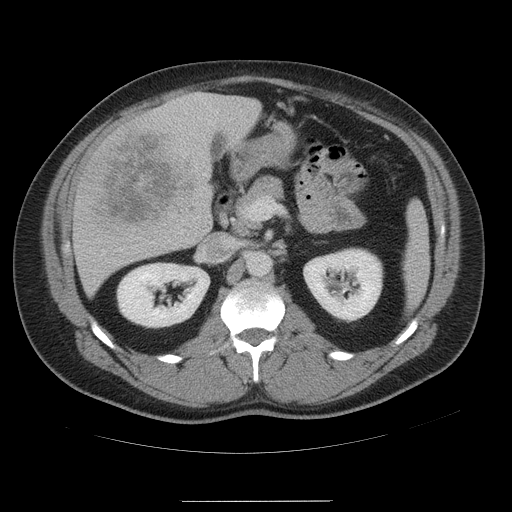
Contrast-enhanced abdominal CT, one axial slice. Position 26 of 54 along the scan axis. 120 kVp. Intravenous contrast given. Soft-tissue window (W 400 / L 40 HU). 512 × 512 image matrix, field of view 436 × 436 mm. Male patient, age 40 years. From the clinical record (not read from this slice): diagnosis: colorectal cancer liver metastases, imaged before liver resection; multiple liver metastases: no; largest metastasis: 15 cm; chemotherapy before resection: no.
Structures marked on this image (manually delineated by an expert):
- liver: bounding box [x1, y1, x2, y2] px = [73, 93, 261, 296]
- planned liver remnant (the part of the liver to remain after resection): [219, 96, 261, 144]
- liver metastasis: [84, 125, 203, 231]